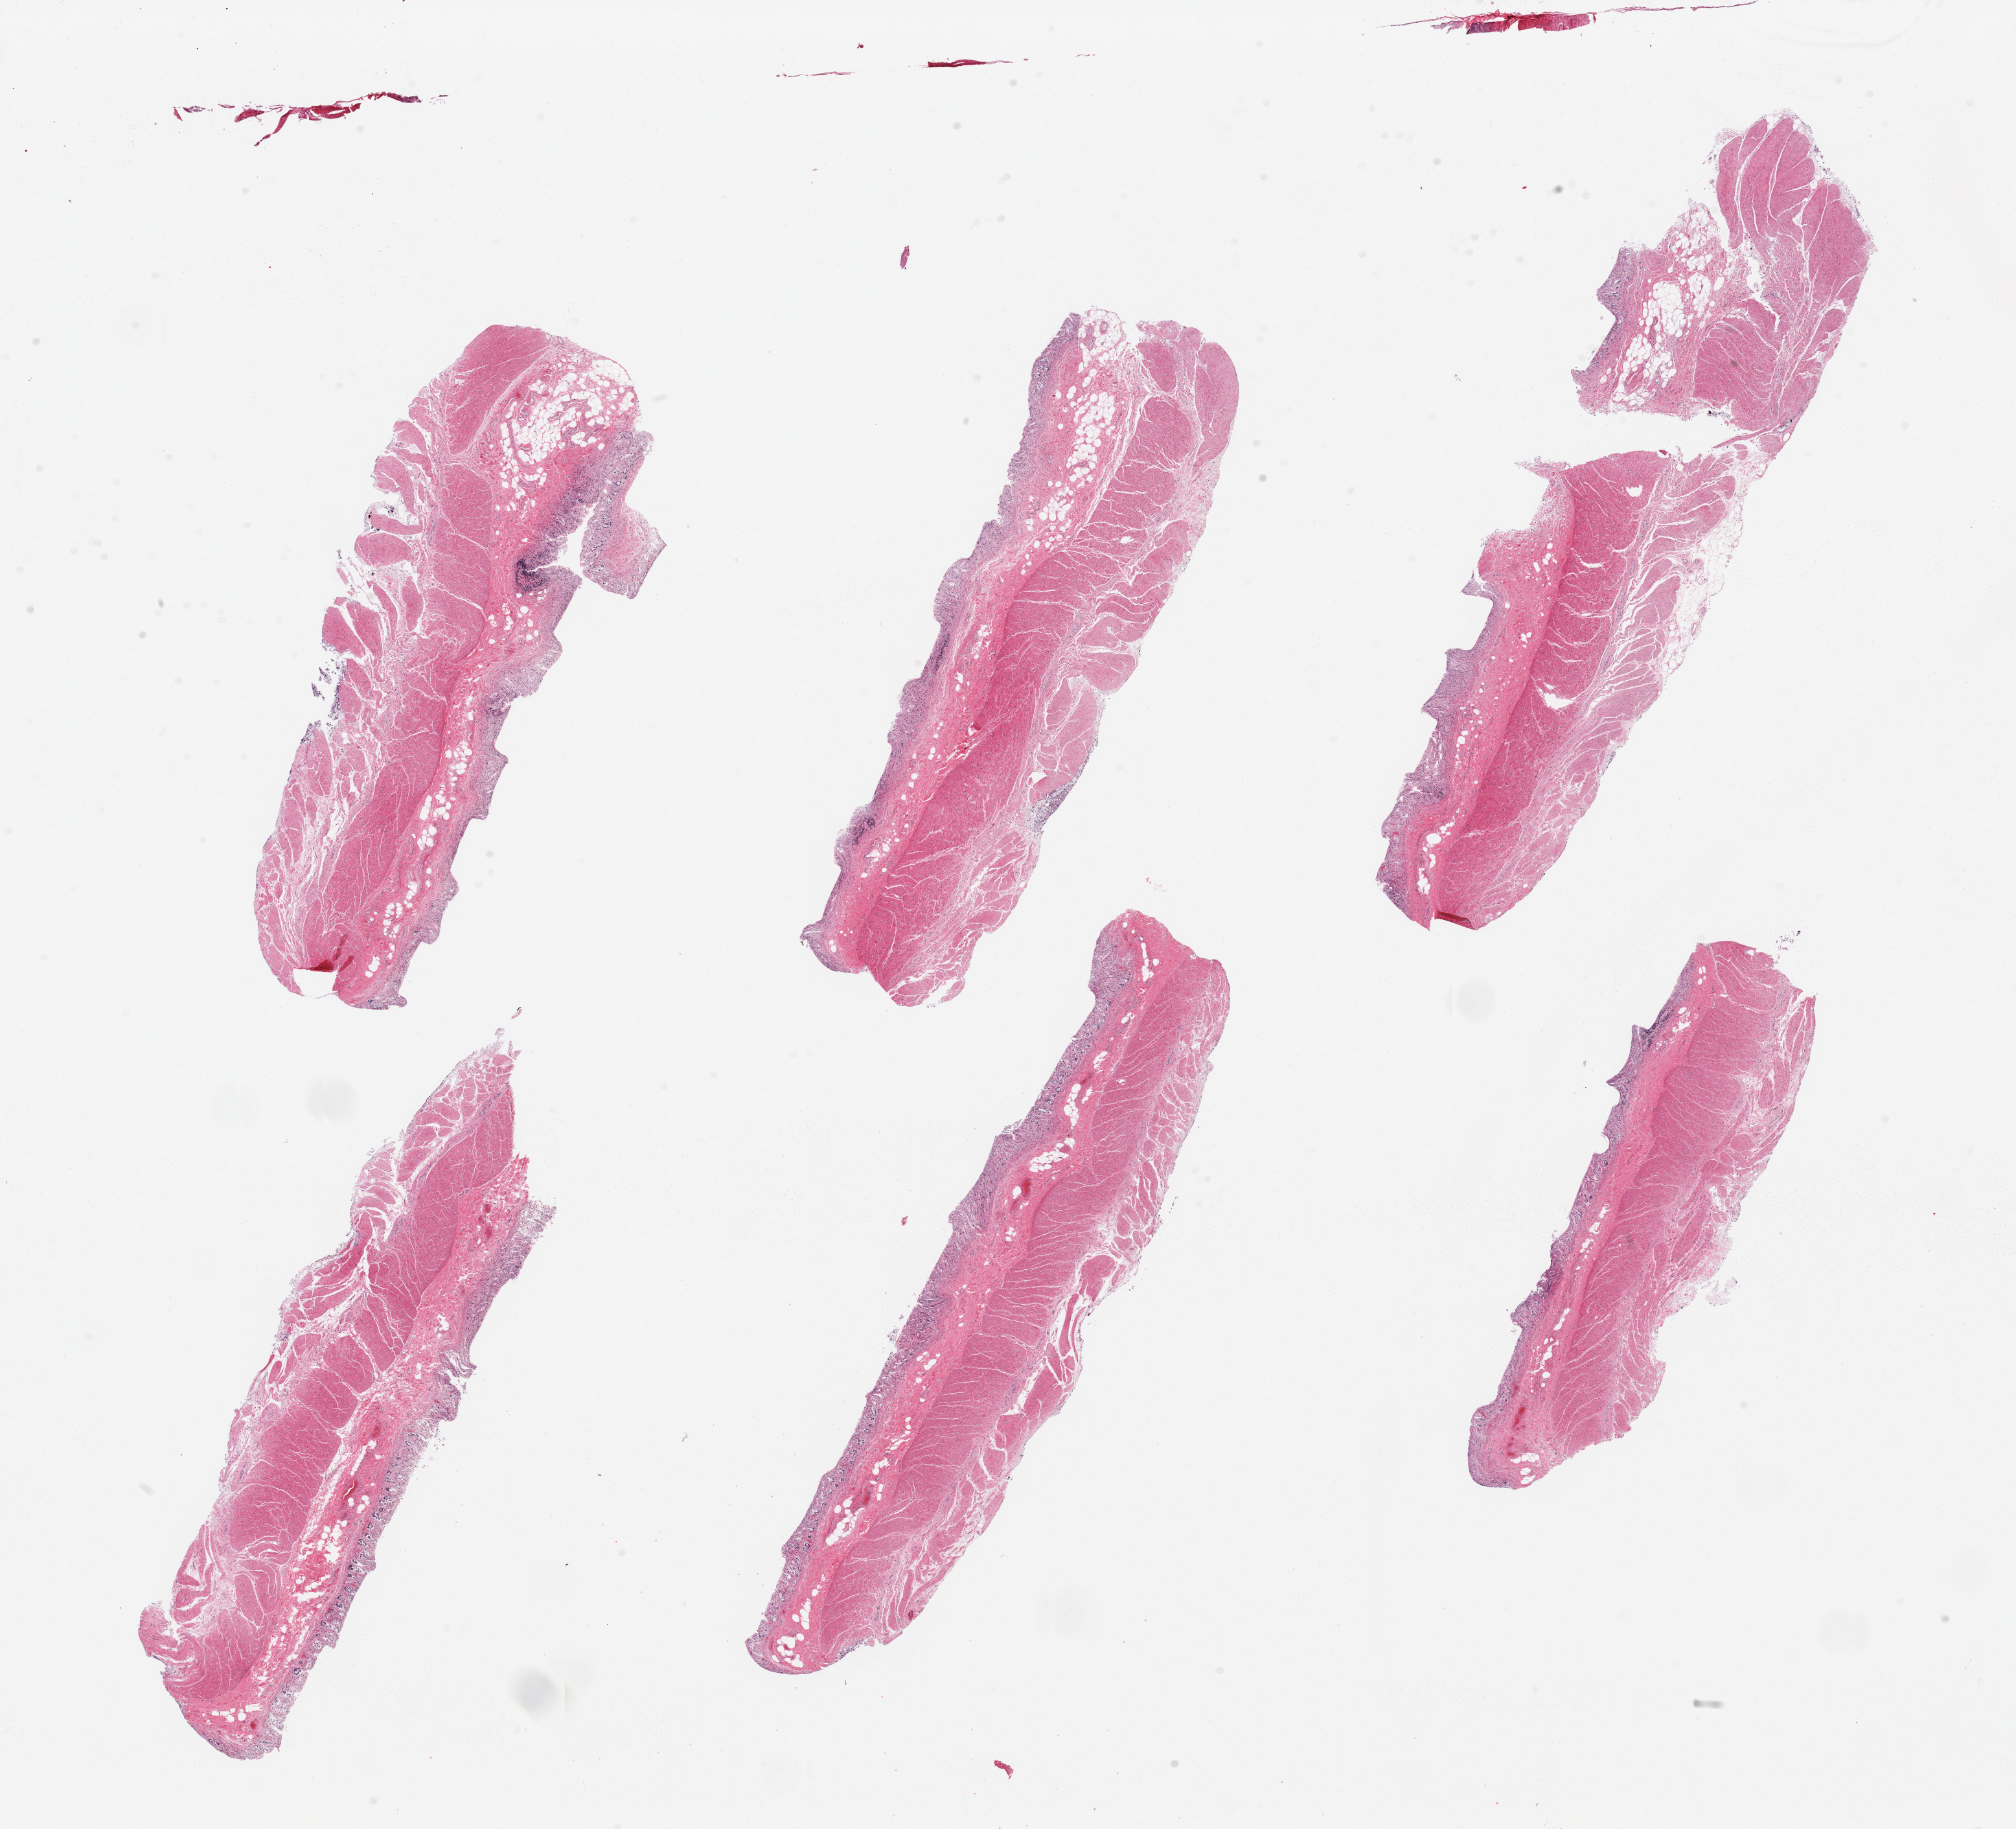
H&E whole-slide image, shown as a low-resolution overview of the whole scanned area (about 24.6 x 22.3 mm, slide scanned at 20x), PAXgene-fixed, paraffin-embedded tissue, target tissue: sigmoid colon, donor tissue sample. Donor sex: male.
Pathologist's review note for this sample: 6 pieces, confirmed target muscularis; trace autolyzed mucosa.